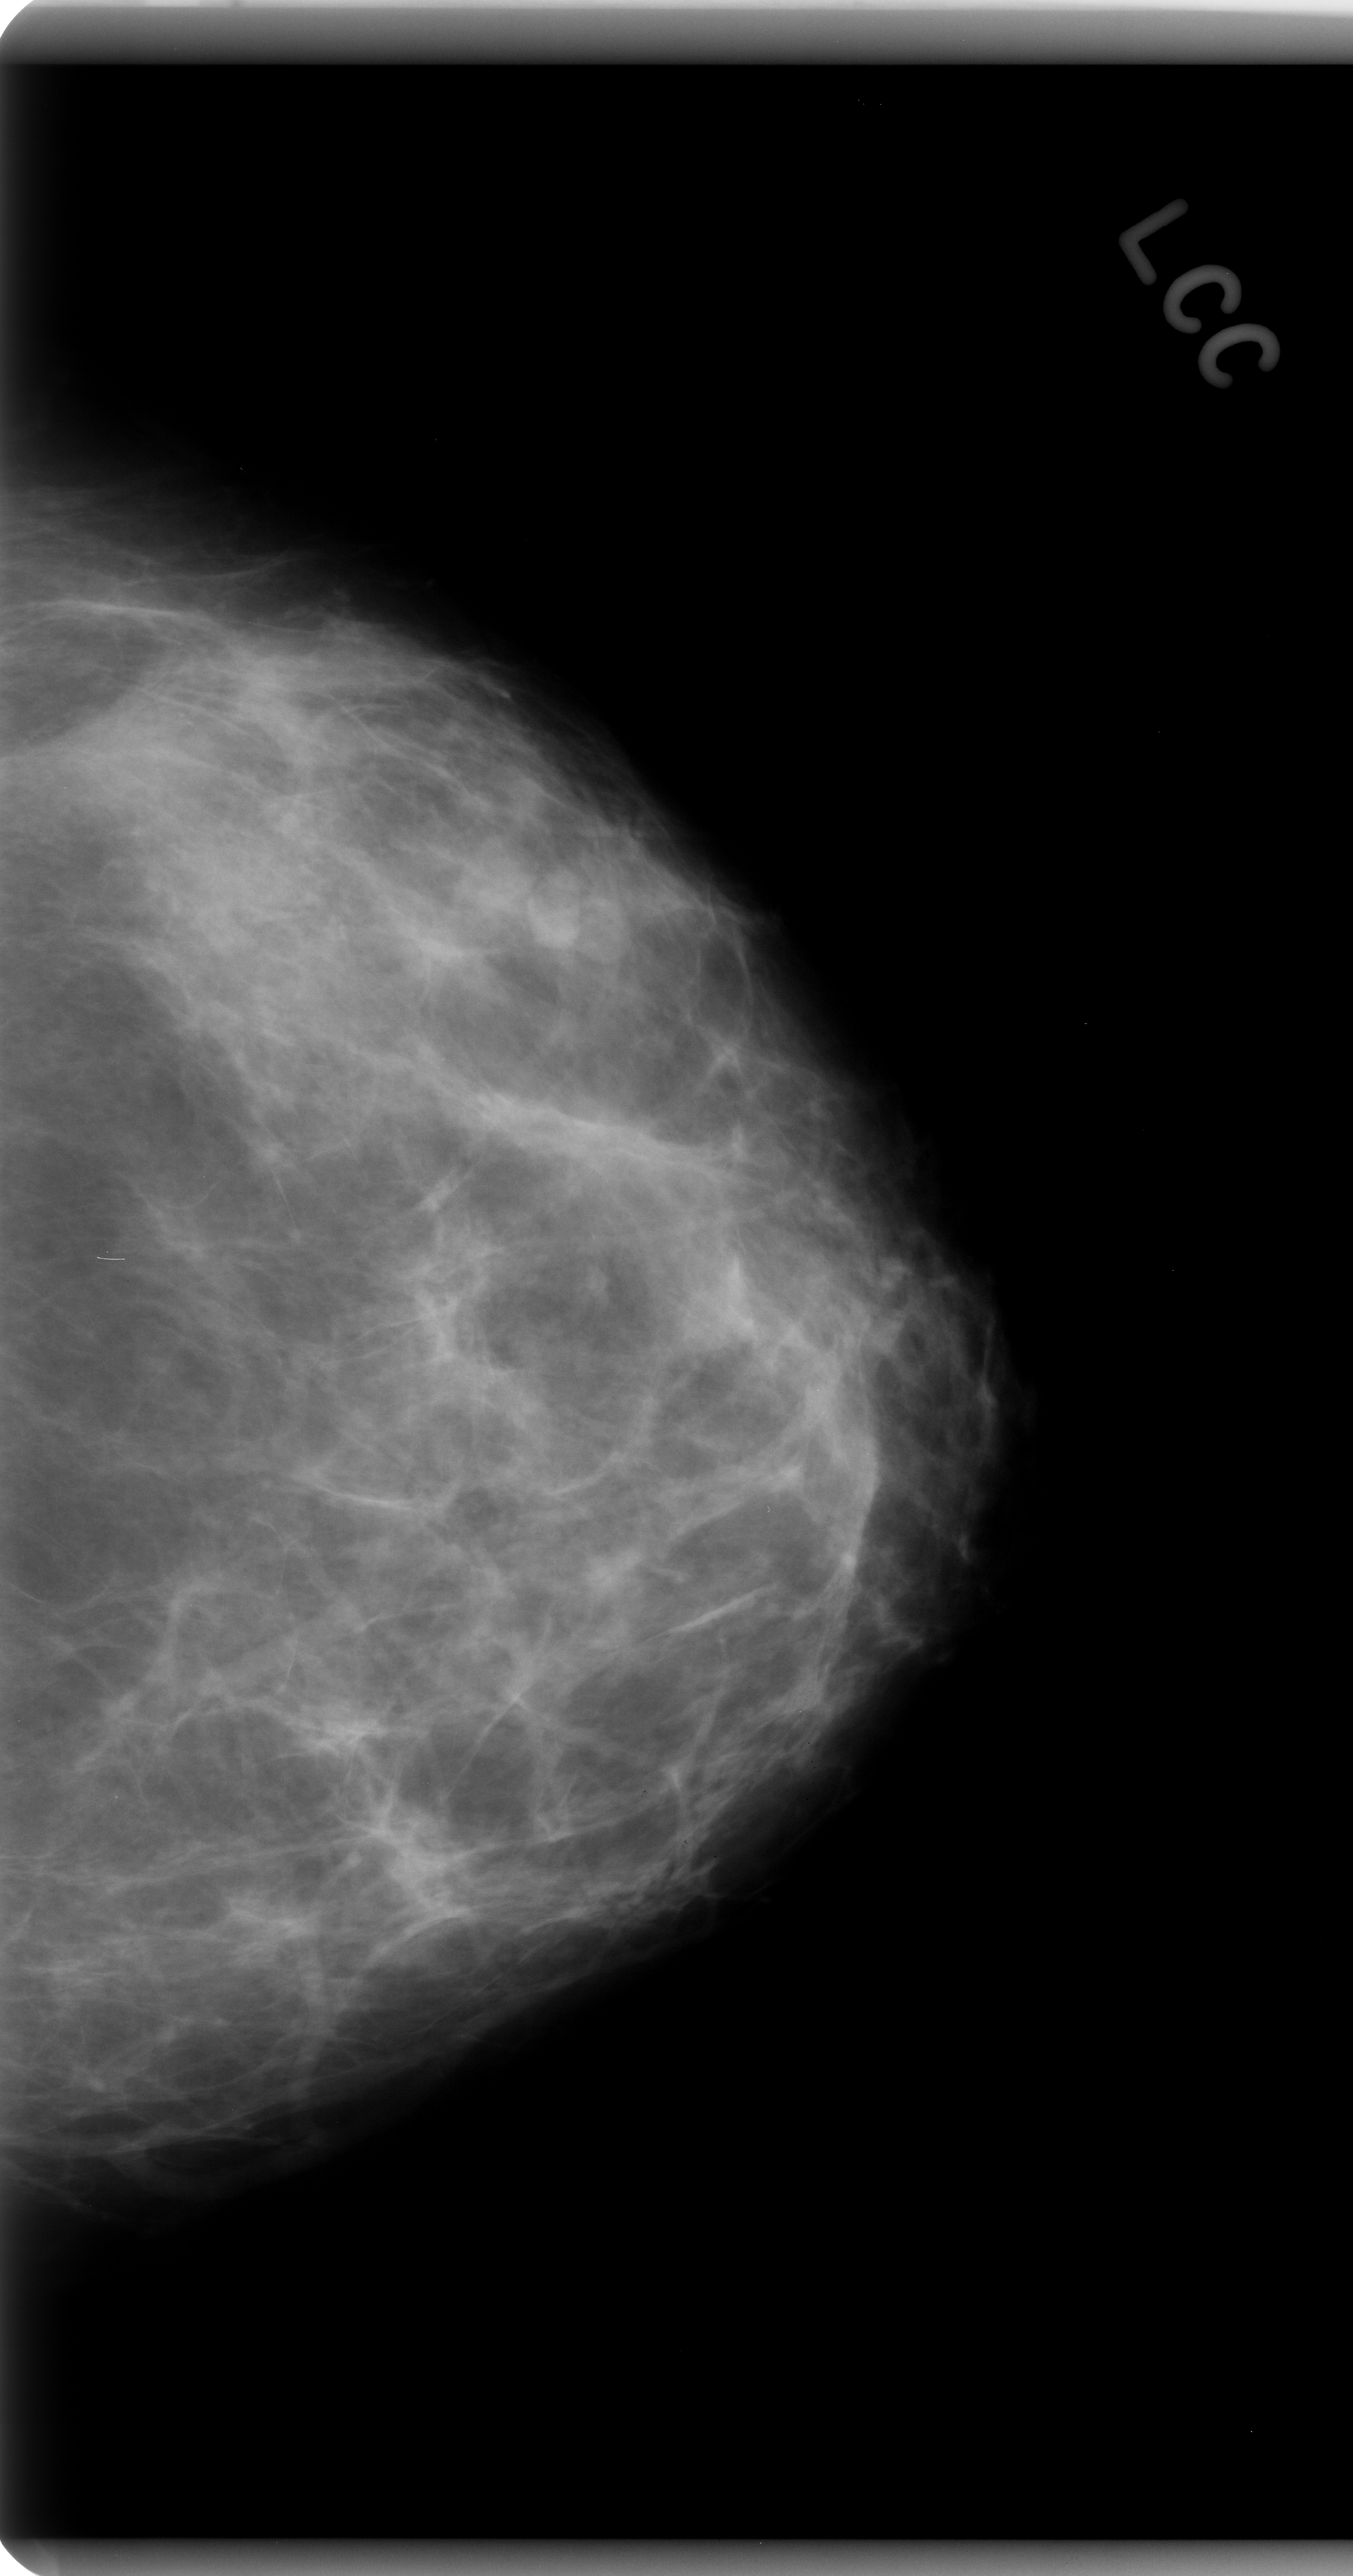
Scanned film-screen mammogram; left breast; CC view; breast composition: scattered fibroglandular densities (BI-RADS density category 2 of 4); 1353 × 2576 image matrix.
Expert-marked regions of interest on this film, with their recorded descriptors:
- mass, shape lobulated, margins circumscribed; BI-RADS assessment category 3; subtlety rating 4 on a 1 (subtle) to 5 (obvious) scale; pathology result (as recorded, not read from the image): benign: box from (x=477, y=852) to (x=586, y=958) px